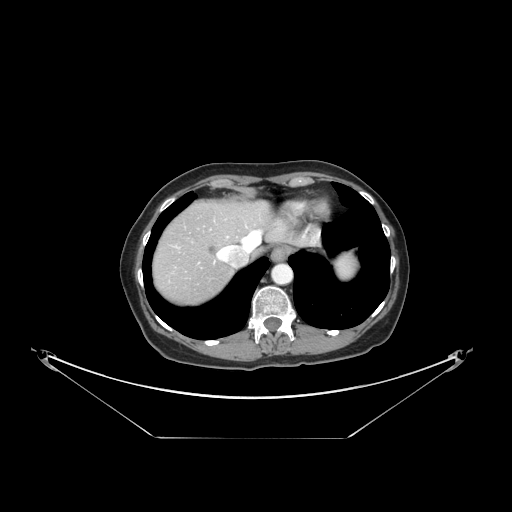
Contrast-enhanced abdominal CT, one axial slice. Position 128 of 148 along the scan axis. Reconstruction kernel STANDARD. 120 kVp. Intravenous contrast given. Soft-tissue window (W 400 / L 40 HU). 2.5 mm slice thickness. 512 × 512 image matrix, field of view 500 × 500 mm. Female patient, age 73 years. Case-level facts recorded for this patient, not image findings: diagnosis: colorectal cancer liver metastases, imaged before liver resection; multiple liver metastases: no; largest metastasis: 1 cm; chemotherapy before resection: yes.
Annotated regions visible in this slice (expert manual segmentation):
- hepatic veins: bounding box <218,228,281,261> (left, top, right, bottom; pixels)
- liver: <154,202,269,305>
- planned liver remnant (the part of the liver to remain after resection): <181,201,274,247>
- liver metastasis: <207,244,218,256>